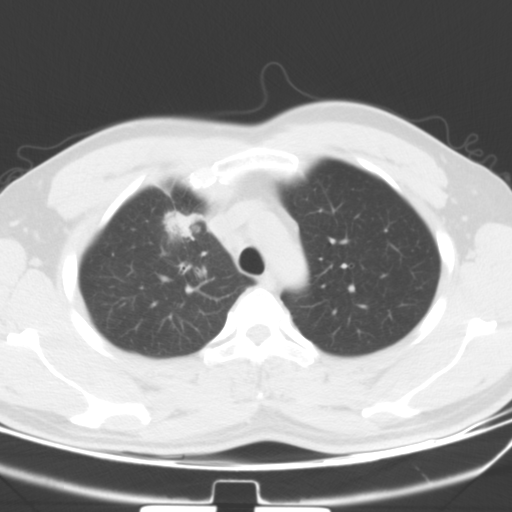
Chest CT, one axial slice. Slice 46 of 60 in the series (ordered by position). 120 kVp. Lung window (W 1500 / L -600 HU). 5 mm slice thickness. 512 × 512 image matrix. Patient: male, 35 years. Case-level facts recorded for this patient, not image findings: clinical TNM (as recorded): T1c N1 M1b.
Structures marked on this image (rectangle marked by the reading radiologist):
- lung tumour (recorded histology: adenocarcinoma): box from (x=167, y=210) to (x=197, y=242) px